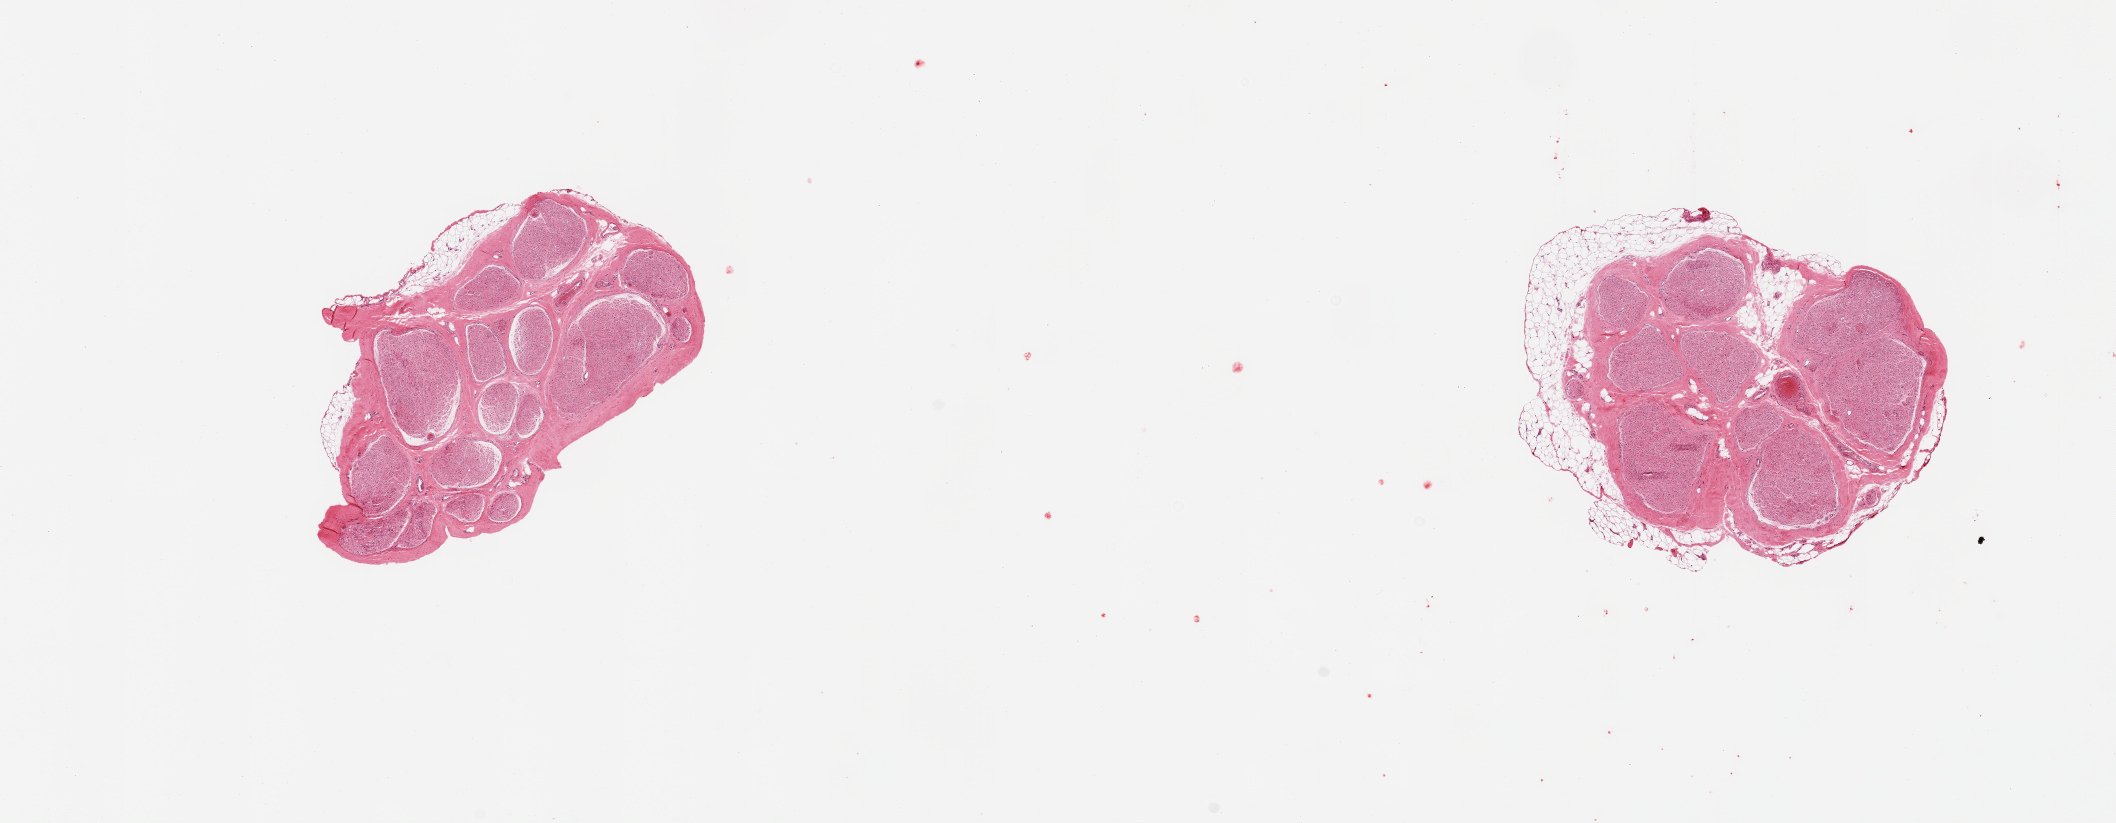
H&E whole-slide image, brightfield — whole scanned area (about 16.7 x 6.5 mm, from a 20x scan) shown as a low-resolution overview. PAXgene-fixed, paraffin-embedded tissue. Section of tibial nerve (target tissue). Tissue donor sample. Donor: female.
- review note (as recorded): 2 pieces; thin rim of external fat occupies 20% & 5%